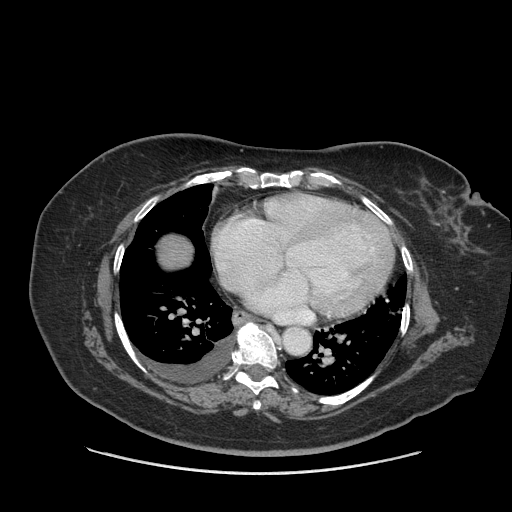
Contrast-enhanced abdominal CT (liver protocol), one axial slice. Reconstruction kernel STANDARD. Soft-tissue window (W 400 / L 40 HU). 2.5 mm slice thickness. 512 × 512 image matrix, field of view 420 × 420 mm. Case-level facts recorded for this patient, not image findings: diagnosis: hepatocellular carcinoma (patient treated with transarterial chemoembolisation; whether this scan precedes or follows treatment is not stated here); TNM stage (as recorded): Stage-I; Child-Pugh class: A; tumour nodularity: uninodular.
Outlined on this slice (semi-automatic segmentation, software-assisted and operator-edited):
- liver parenchyma outside the tumour (the mass and vessels are separate outlines, so this box may not span the whole liver): bounding box <158,234,192,268> (left, top, right, bottom; pixels)